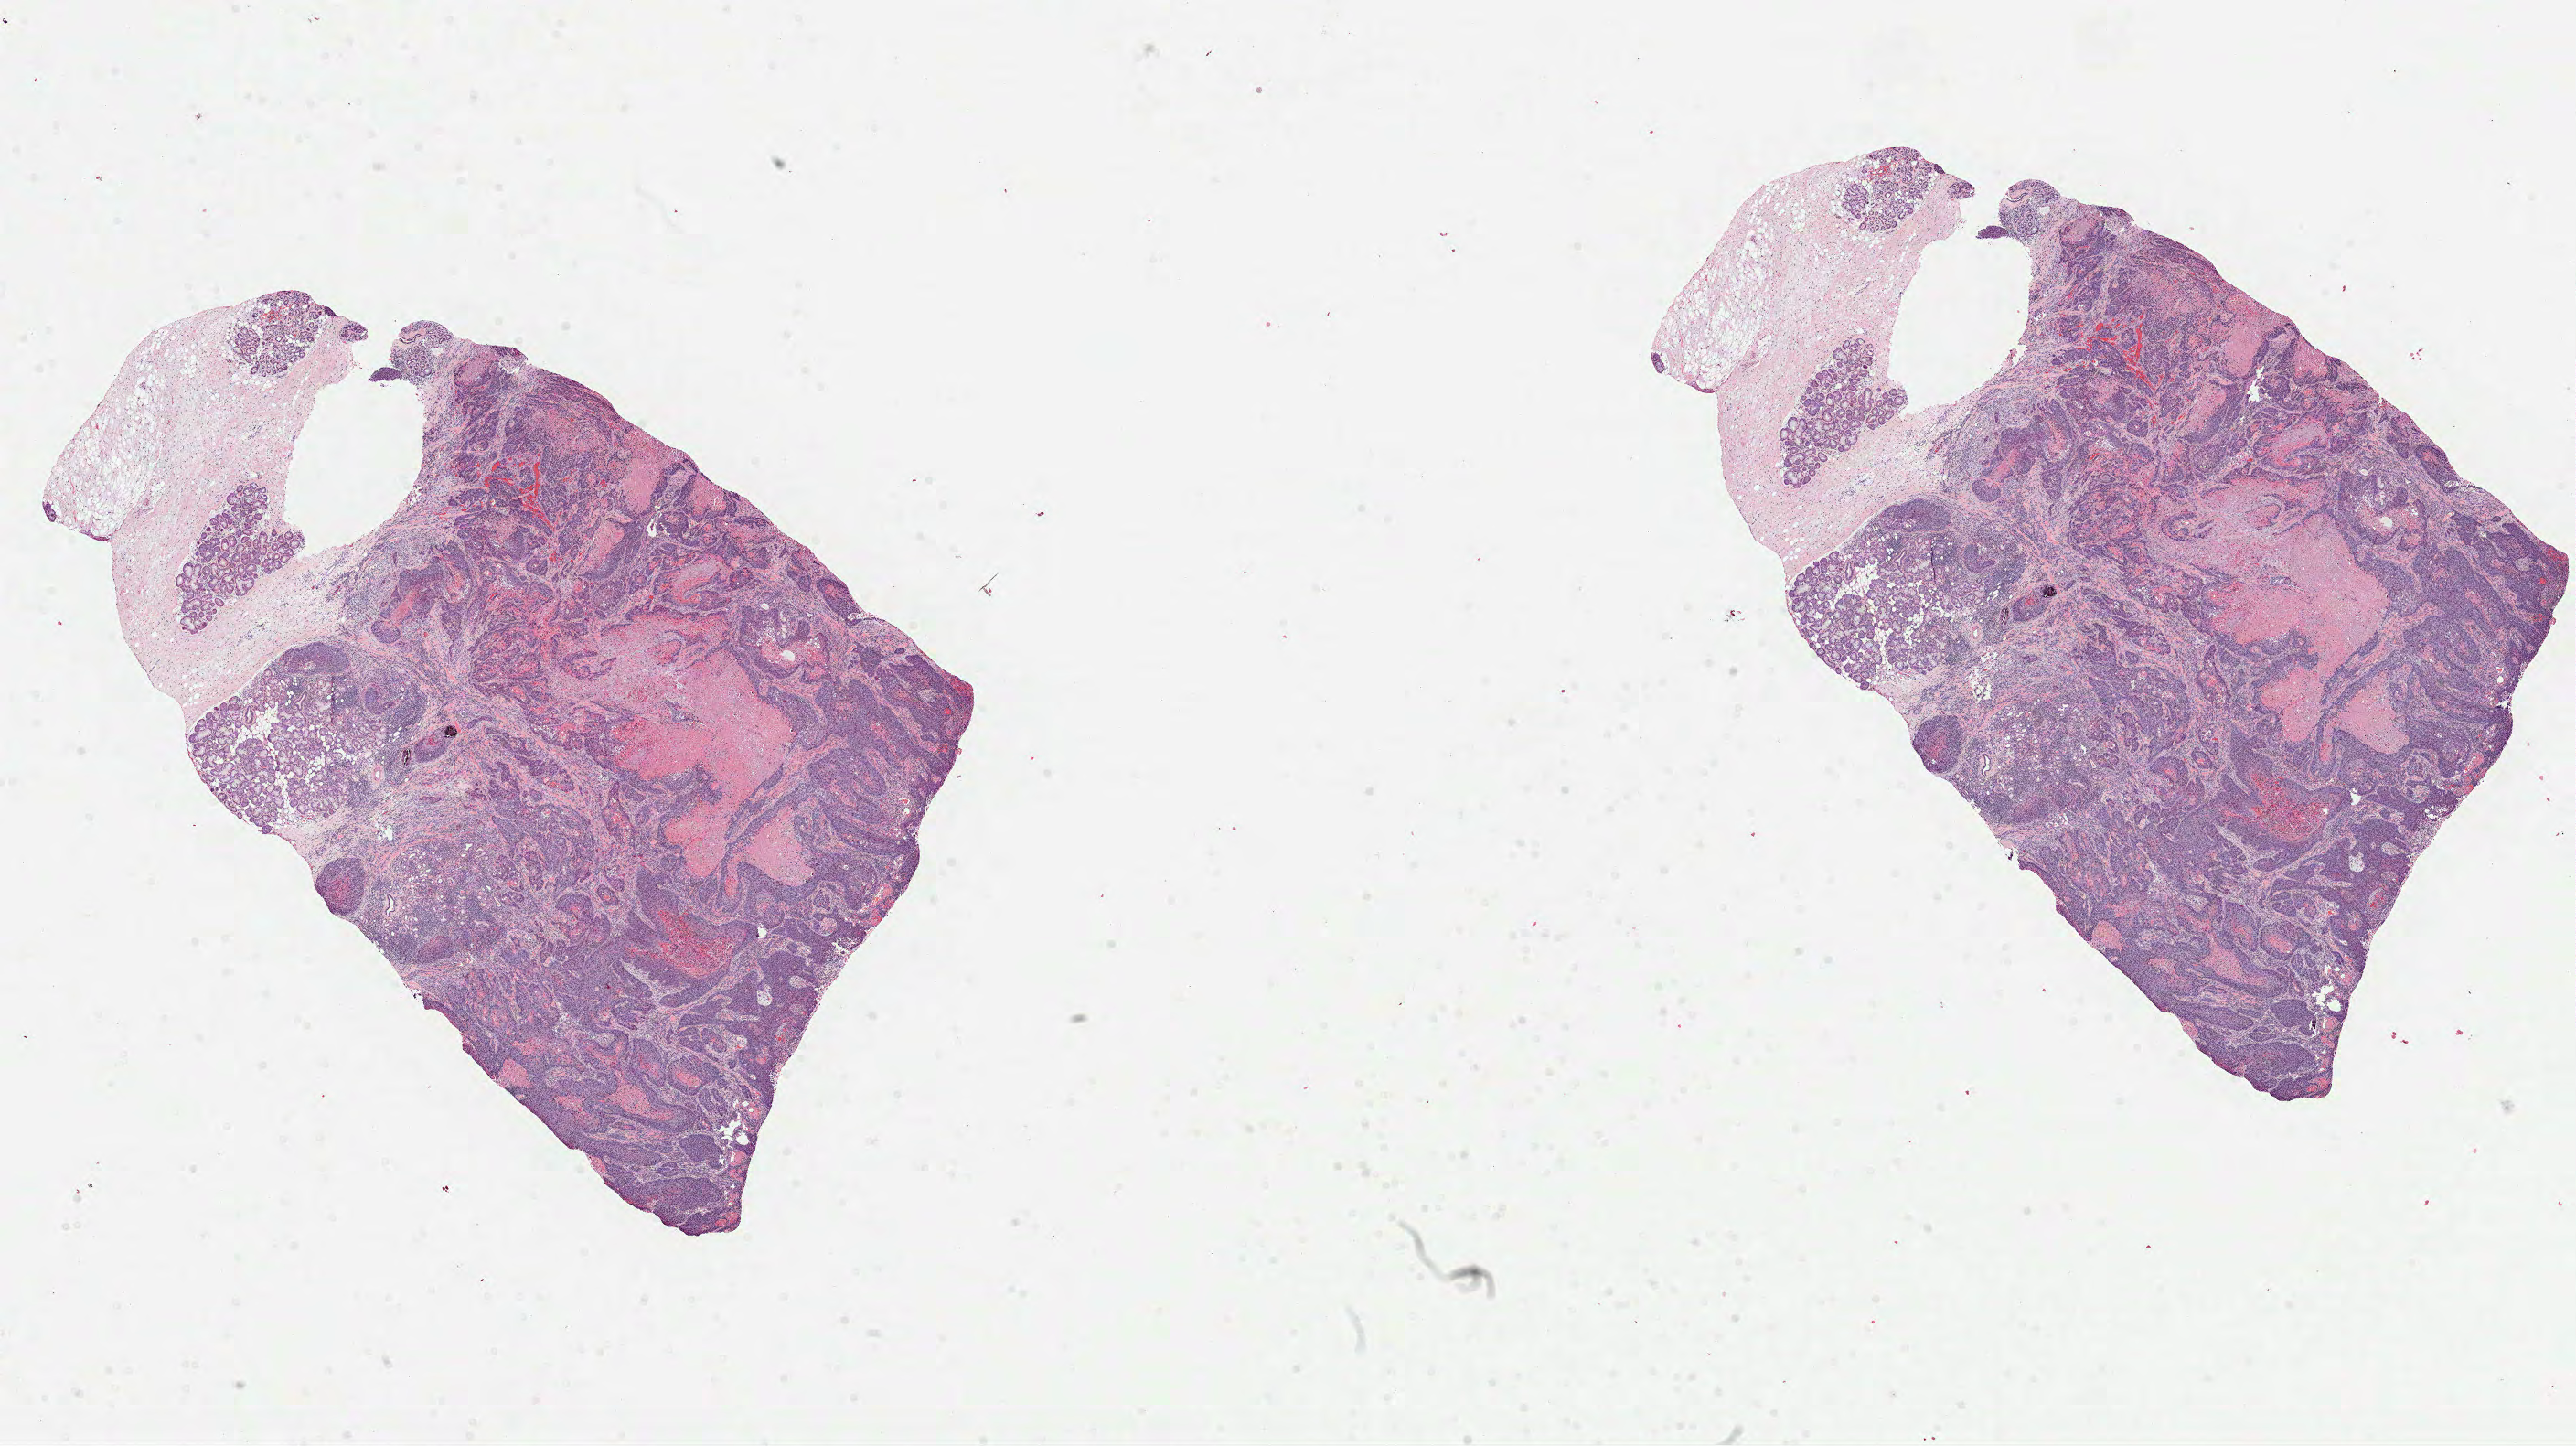
H&E whole-slide image, low-resolution overview of the scanned area, about 22.7 x 12.8 mm (slide scanned at 40x). FFPE section. Primary tumour sample from the head and neck. Male, age 61 years at initial diagnosis. Histologic grade: G2 (moderately differentiated).
AJCC pathologic stage: IVA (7th edition). Lymph nodes positive (case pathology): 3 of 48 examined. Histologic diagnosis: Squamous cell carcinoma, NOS (larynx, NOS). TNM: T3 N2b.